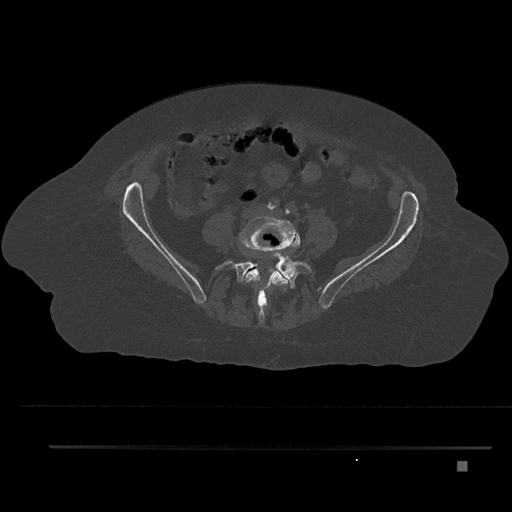
CT including the spine, one axial slice. Slice 56 of 797 in the series (ordered by position). 120 kVp. Bone window (W 1800 / L 400 HU). 0.5 mm slice thickness. 512 × 512 image matrix, field of view 437 × 437 mm. Patient: female, 76 years. Case-level facts recorded for this patient, not image findings: primary cancer: lung; vertebrae with lytic lesions (as recorded): T11, L3.
Structures marked on this image (semi-automatic segmentation, software-assisted and operator-edited):
- L4 vertebra: box from (x=240, y=215) to (x=300, y=313) px
- L5 vertebra: (x=215, y=252)–(x=312, y=322)